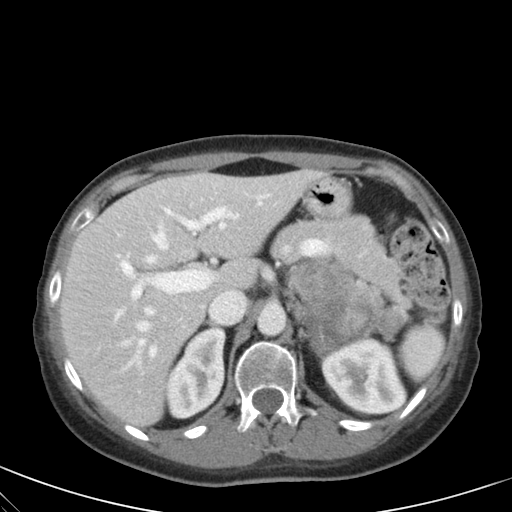
Contrast-enhanced abdominal CT, one axial slice. Slice 38 of 59 in the series (ordered by position). Intravenous contrast given. Soft-tissue window (W 400 / L 40 HU). 512 × 512 image matrix, field of view 350 × 350 mm. Patient: female, 28 years. Case-level facts recorded for this patient, not image findings: diagnosis: adrenocortical carcinoma; tumour side: left adrenal; tumour size at pathology: 7 cm; Ki-67 index: 40 %; stage (as recorded): 4.
Structures marked on this image (semi-automatic segmentation, software-assisted and operator-edited):
- mass: box from (x=290, y=263) to (x=402, y=353) px